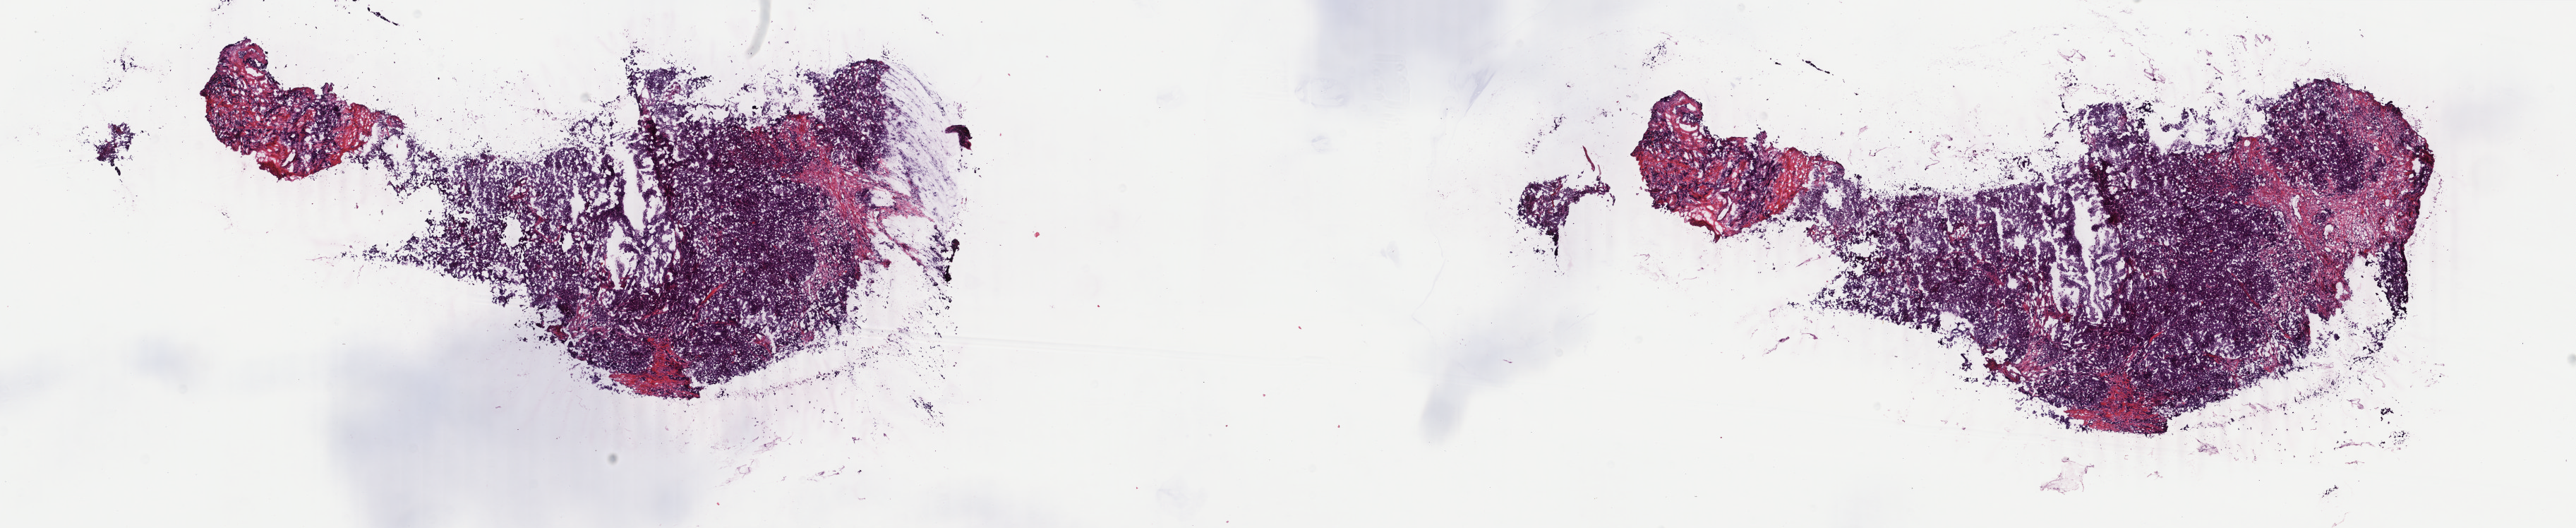
H&E whole-slide image — a low-resolution overview of the entire scanned area, about 29.0 x 5.9 mm (slide scanned at 40x); frozen section; sample: primary tumour, breast. Patient: female, age at initial diagnosis 67 years. Slide review estimates, as recorded: tumour cells 85%, tumour nuclei 85%, normal cells 0%, stromal cells 15%, necrosis 0%. Infiltration values recorded for this section: lymphocyte infiltration 2%, monocyte infiltration 0%, neutrophil infiltration 0%.
Lymph nodes positive (case pathology): 1 of 36 examined. AJCC pathologic stage: IIB. Pathologic diagnosis: Infiltrating duct mixed with other types of carcinoma.